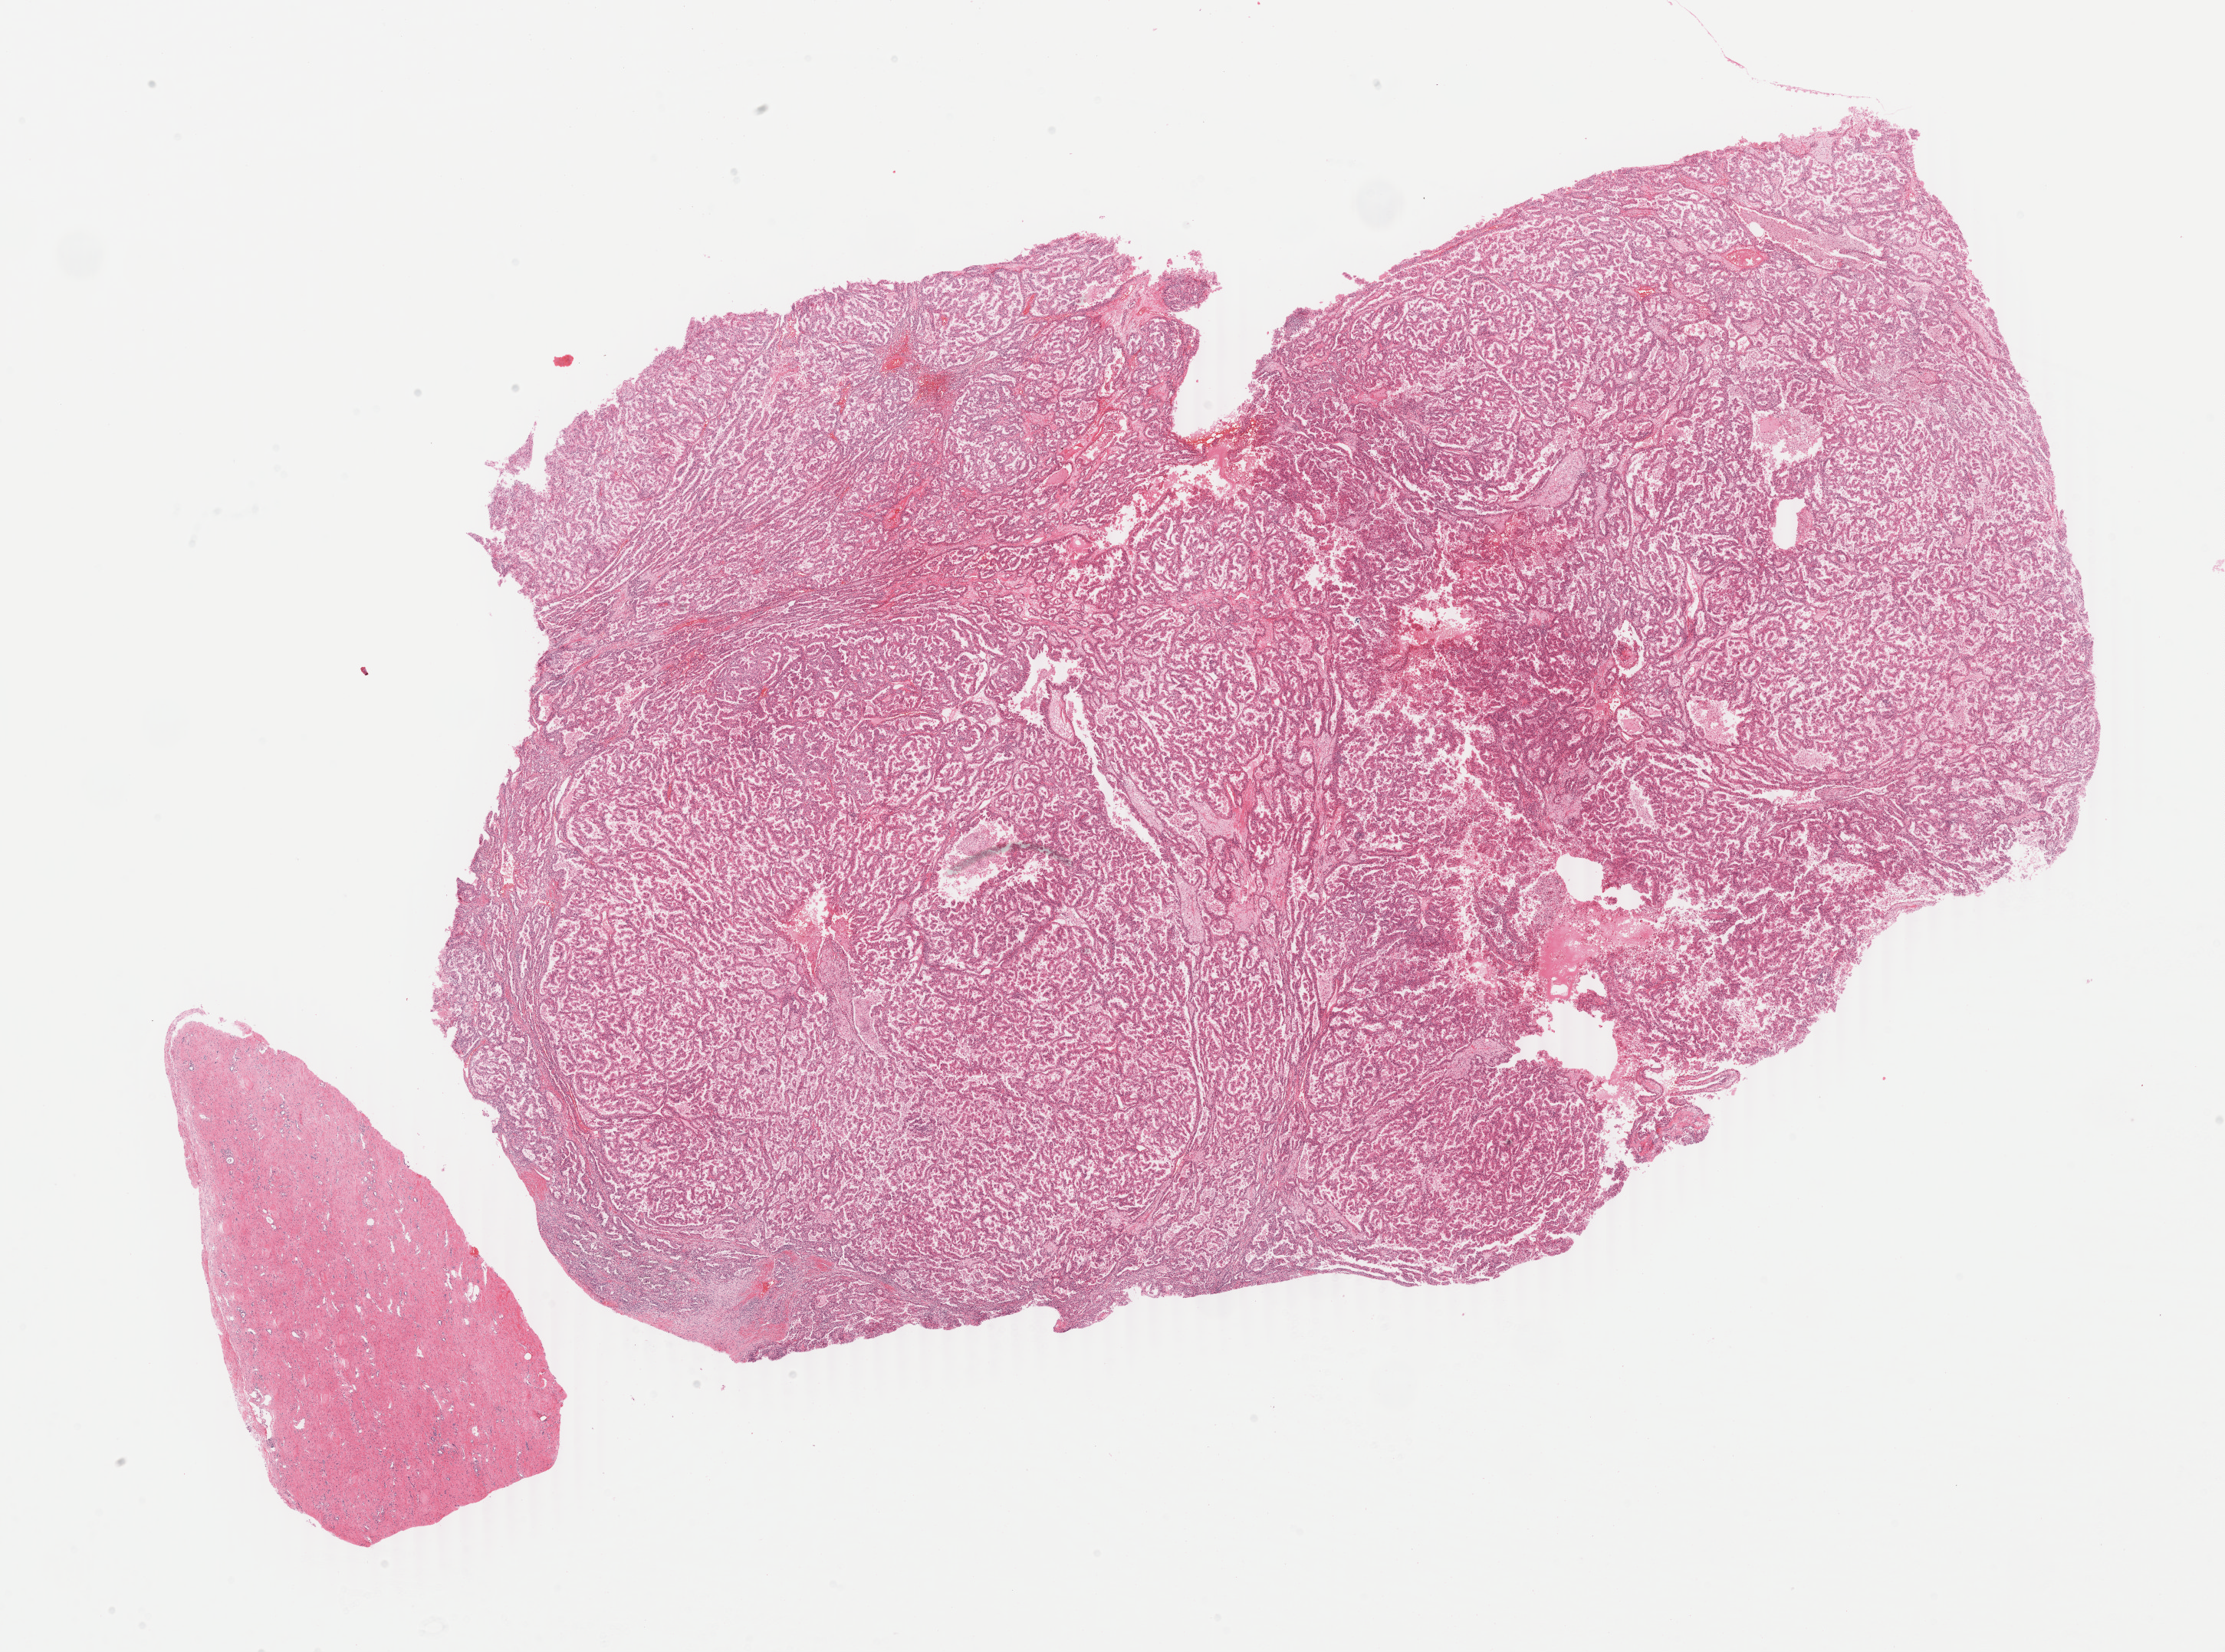
Digitized H&E tissue section (whole slide) — shown as a low-resolution overview of the whole scanned area (about 23.1 x 17.1 mm, acquisition: 40x scan); formalin-fixed paraffin-embedded (FFPE) diagnostic section; primary tumour sample from the kidney. Patient: male, age at initial diagnosis 55 years.
* diagnosis: Papillary adenocarcinoma, NOS
* lymph nodes positive (case pathology): 0 of 33 examined
* AJCC pathologic stage: II (6th edition)